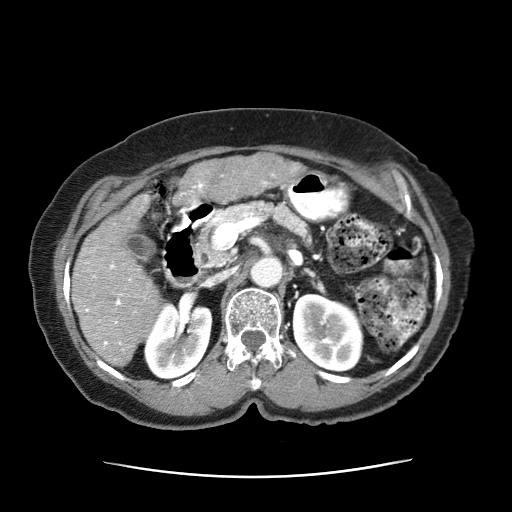
Contrast-enhanced abdominal CT (liver protocol), one axial slice. Slice 22 of 63 in the series (ordered by position). Reconstruction kernel STANDARD. Intravenous contrast given. Soft-tissue window (W 400 / L 40 HU). 512 × 512 image matrix, field of view 360 × 360 mm. Female patient, age 79 years. Case-level facts recorded for this patient, not image findings: diagnosis: hepatocellular carcinoma (patient treated with transarterial chemoembolisation; whether this scan precedes or follows treatment is not stated here); TNM stage (as recorded): Stage-II; Child-Pugh class: B; tumour differentiation: well differentiated; tumour nodularity: multinodular.
Outlined on this slice (semi-automatically segmented with operator editing):
- abdominal aorta: box from (x=251, y=251) to (x=283, y=286) px
- liver parenchyma outside the tumour (the mass and vessels are separate outlines, so this box may not span the whole liver): (x=70, y=193)–(x=165, y=369)
- mass: (x=174, y=154)–(x=300, y=201)
- liver vessels: (x=85, y=264)–(x=145, y=347)